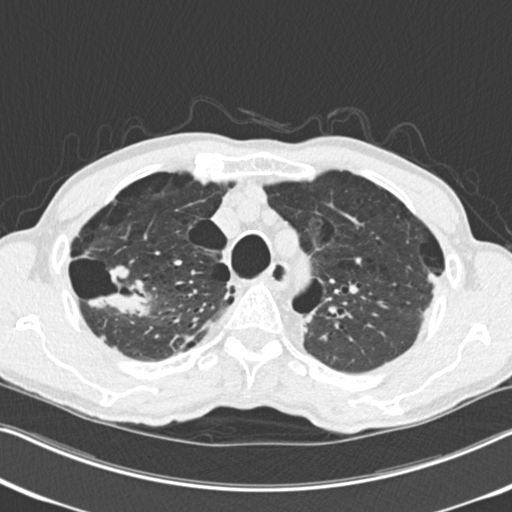
Low-dose screening chest CT, one axial slice; slice 197 of 251 in the series (ordered by position); 120 kVp; lung window (W 1500 / L -600 HU); 2 mm slice thickness; 512 × 512 image matrix, field of view 334 × 334 mm.
Outlined on this slice (outlined manually by an expert reader):
- lesion 1 (tumor, upper lobe of right lung): bounding box <89,266,151,316> (left, top, right, bottom; pixels)